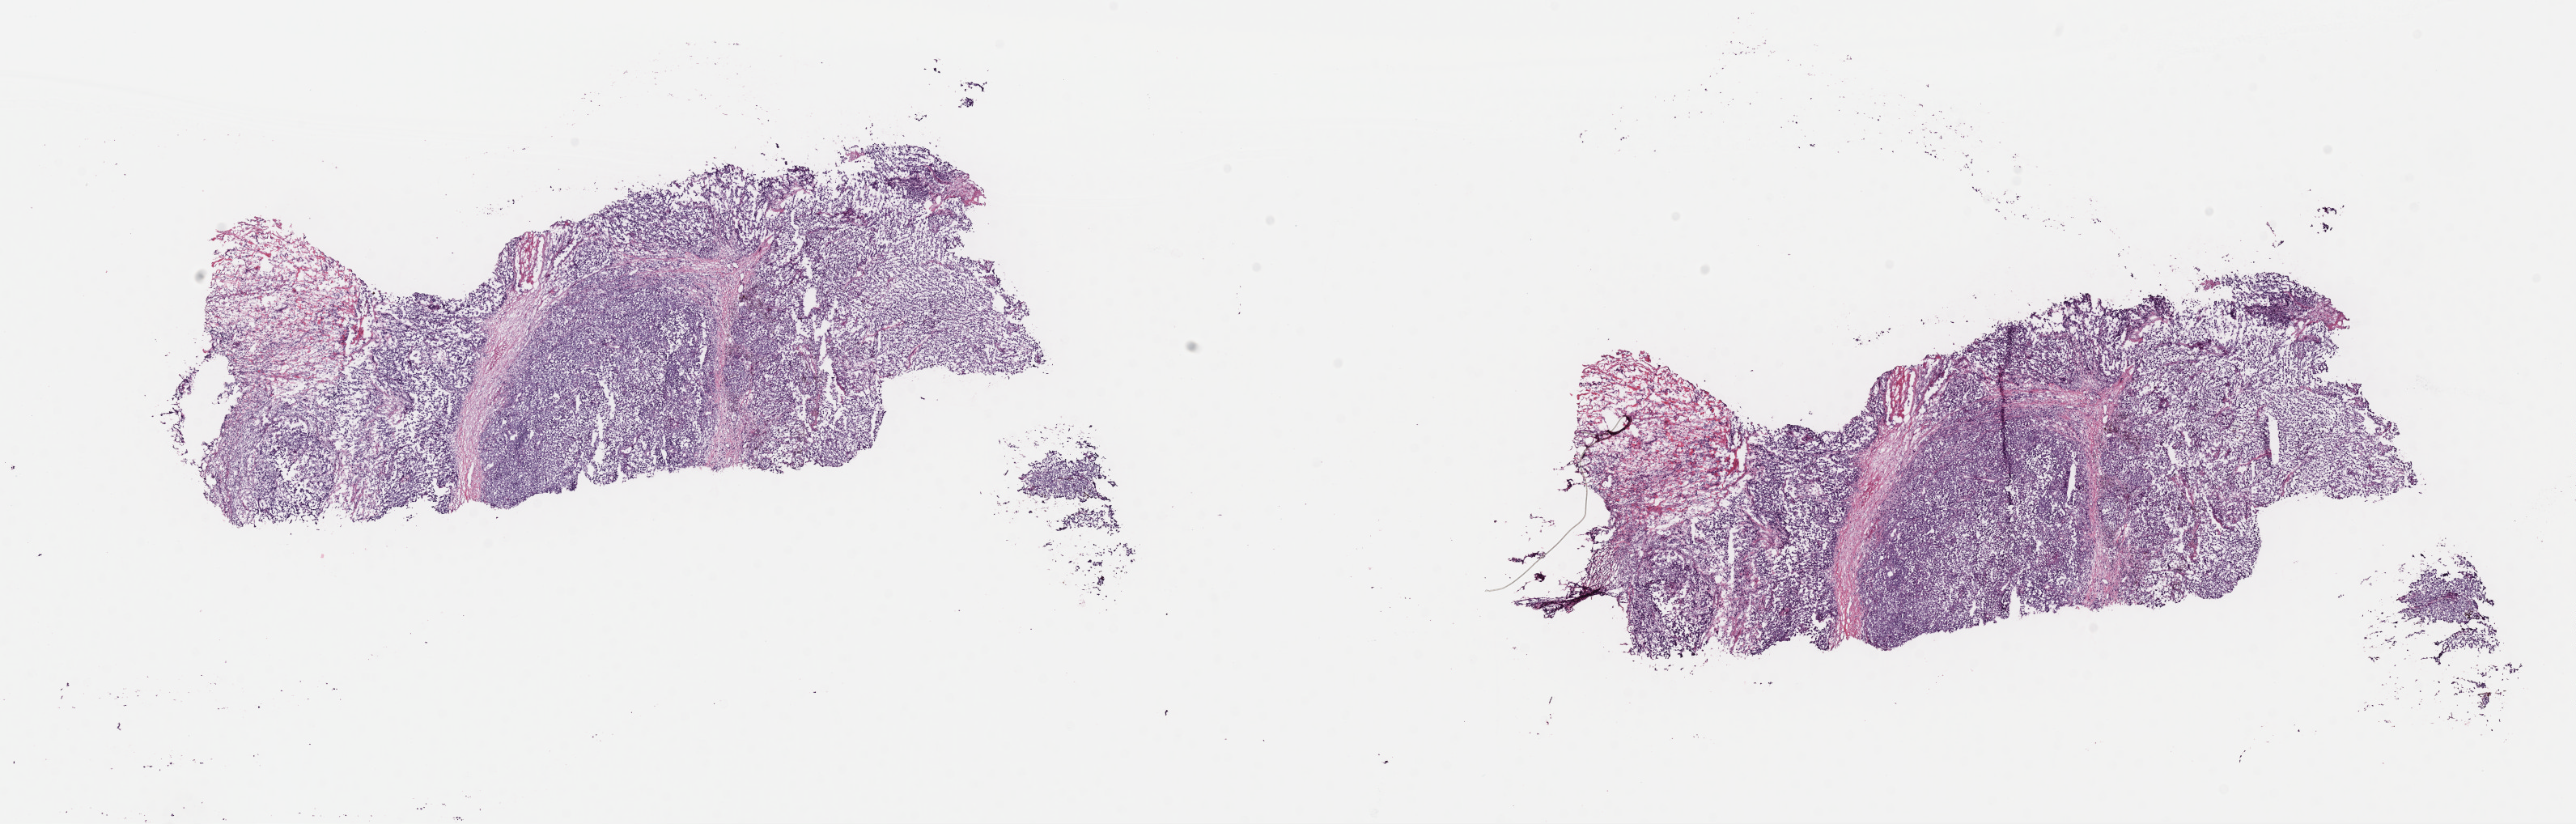
Hematoxylin and eosin (H&E) stained whole-slide image, a low-resolution overview of the entire scanned area, about 25.1 x 8.0 mm (from a 40x scan); frozen section; metastatic tumour sample, sampled site not recorded. Female patient; age at initial diagnosis 34 years. Pathologist review of this section (percent, as recorded): tumour cells 70%, tumour nuclei 70%, normal cells 0%, stromal cells 28%, necrosis 2%. Inflammatory infiltration, as recorded: lymphocyte infiltration 2%, monocyte infiltration 1%, neutrophil infiltration 0%.
* this section: metastatic tumour tissue
* patient diagnosis: Malignant melanoma, NOS